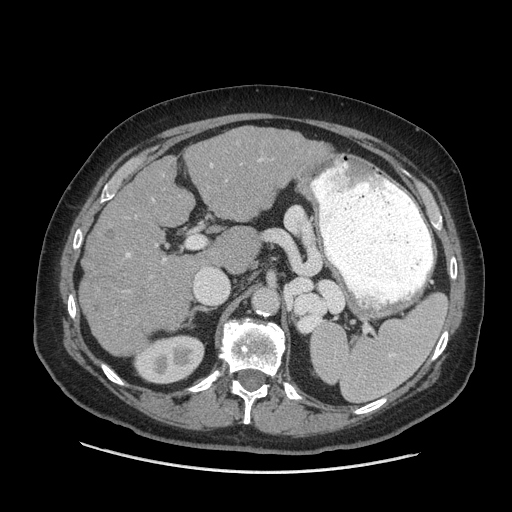
Contrast-enhanced abdominal CT (liver protocol), one axial slice. Slice 36 of 77 in the series (ordered by position). 140 kVp. Soft-tissue window (W 400 / L 40 HU). 2.5 mm slice thickness. 512 × 512 image matrix, field of view 420 × 420 mm. Case-level facts recorded for this patient, not image findings: diagnosis: hepatocellular carcinoma (patient treated with transarterial chemoembolisation; whether this scan precedes or follows treatment is not stated here); TNM stage (as recorded): Stage-I; Child-Pugh class: A; tumour differentiation: well differentiated; tumour nodularity: uninodular.
Structures marked on this image (semi-automatically segmented with operator editing):
- liver parenchyma outside the tumour (the mass and vessels are separate outlines, so this box may not span the whole liver): bounding box <80,126,332,356> (left, top, right, bottom; pixels)
- liver vessels: <126,158,263,261>